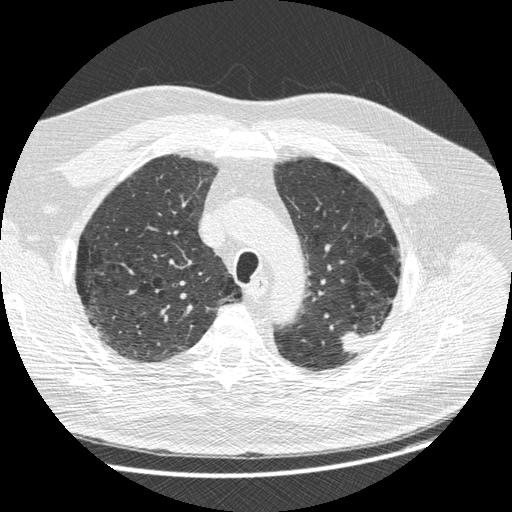
Low-dose screening chest CT, one axial slice; position 203 of 258 along the scan axis; 120 kVp; lung window (W 1500 / L -600 HU); 1.25 mm slice thickness; 512 × 512 image matrix, field of view 370 × 370 mm.
Outlined on this slice (manually delineated by an expert):
- lesion 1 (tumor, upper lobe of left lung): bounding box <341,331,373,354> (left, top, right, bottom; pixels)